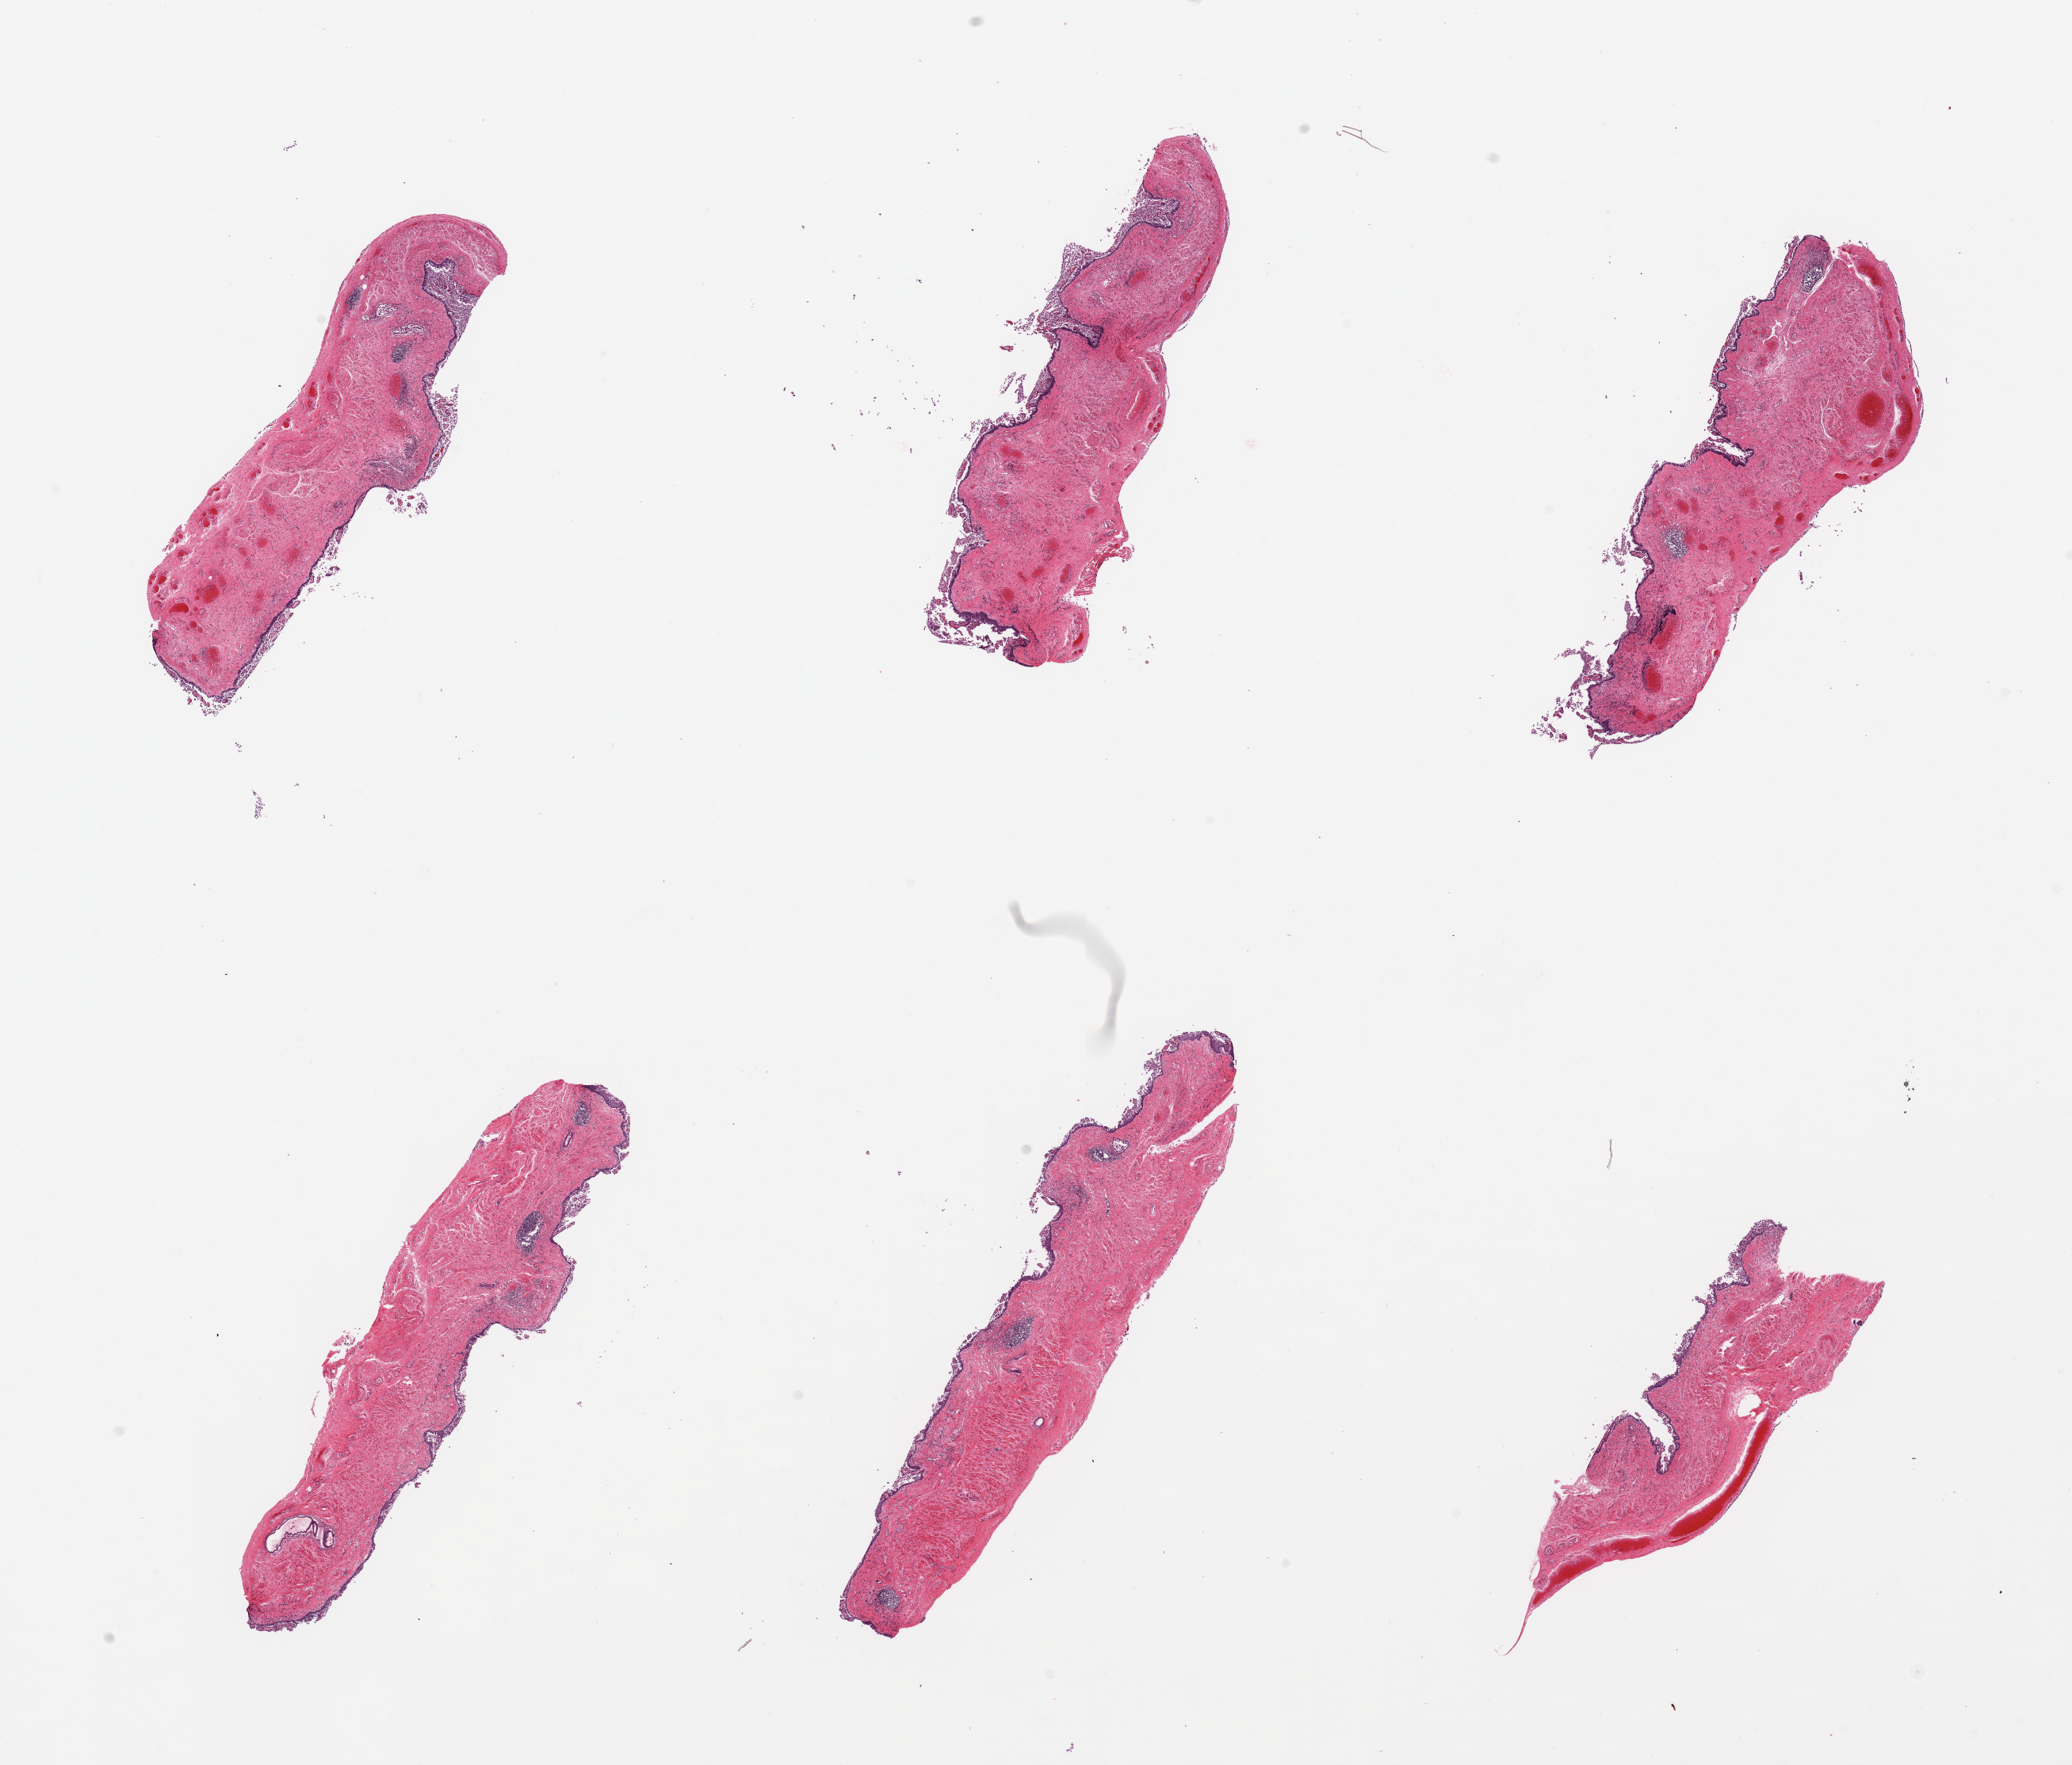
Whole-slide image, H&E stain — low-resolution overview of the scanned area, about 20.7 x 17.6 mm (slide scanned at 20x), PAXgene-fixed paraffin-embedded (PFPE) section, sampled site (target tissue): esophageal mucous membrane, donor tissue sample. Male donor.
• review note (as recorded): 6 pieces; severe sloughing of epithelium; chronic esophagitis